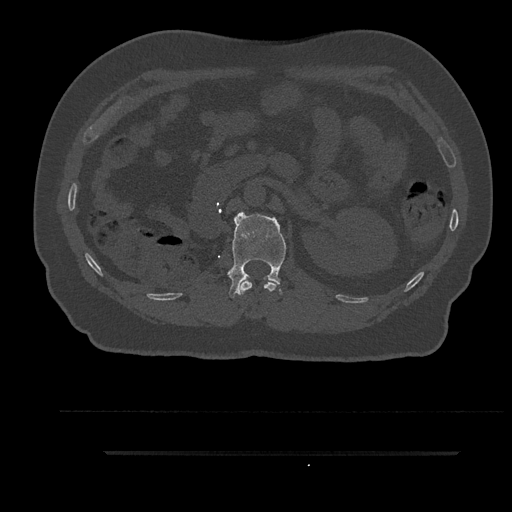
CT including the spine, one axial slice. Slice 190 of 797 in the series (ordered by position). Bone window (W 1800 / L 400 HU). 512 × 512 image matrix, field of view 432 × 432 mm. Patient: male, 63 years. From the clinical record (not read from this slice): primary cancer: renal.
Annotated regions visible in this slice (semi-automatic segmentation, software-assisted and operator-edited):
- L1 vertebra: box from (x=228, y=212) to (x=286, y=298) px
- T12 vertebra: (x=240, y=280)–(x=279, y=295)